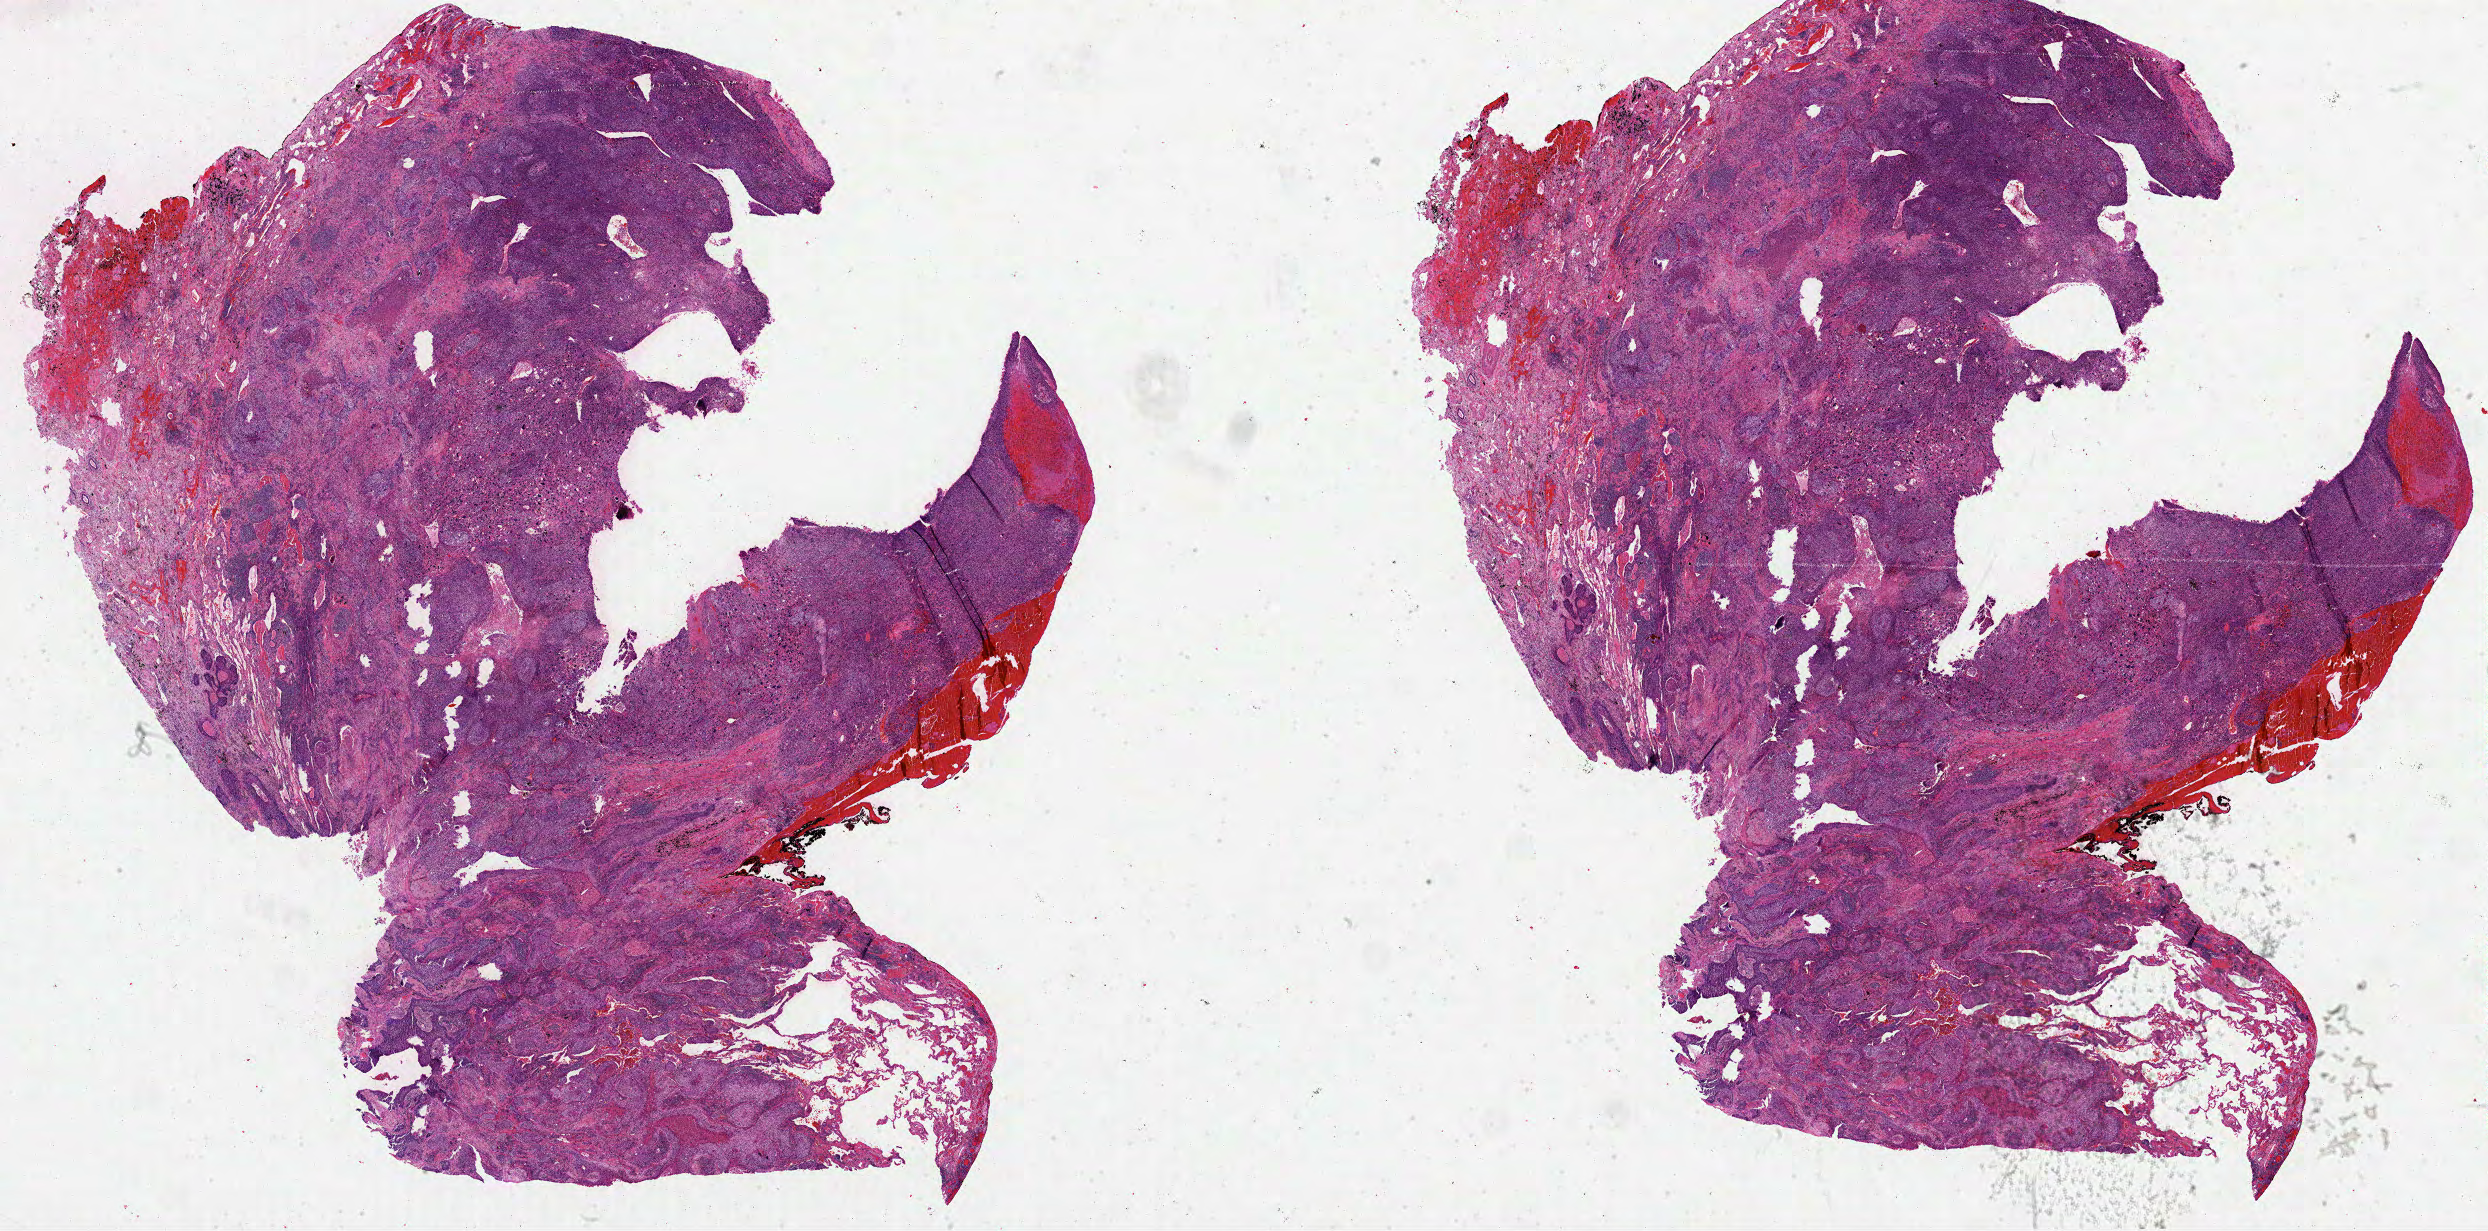
H&E-stained whole-slide image — low-resolution overview of the scanned area, about 40.1 x 19.9 mm (acquisition: 40x scan), formalin-fixed paraffin-embedded (FFPE) diagnostic section, lung, primary tumour sample. Female, age 76 years at initial diagnosis.
AJCC pathologic stage: IB (5th edition). Histologic diagnosis: Squamous cell carcinoma, NOS.